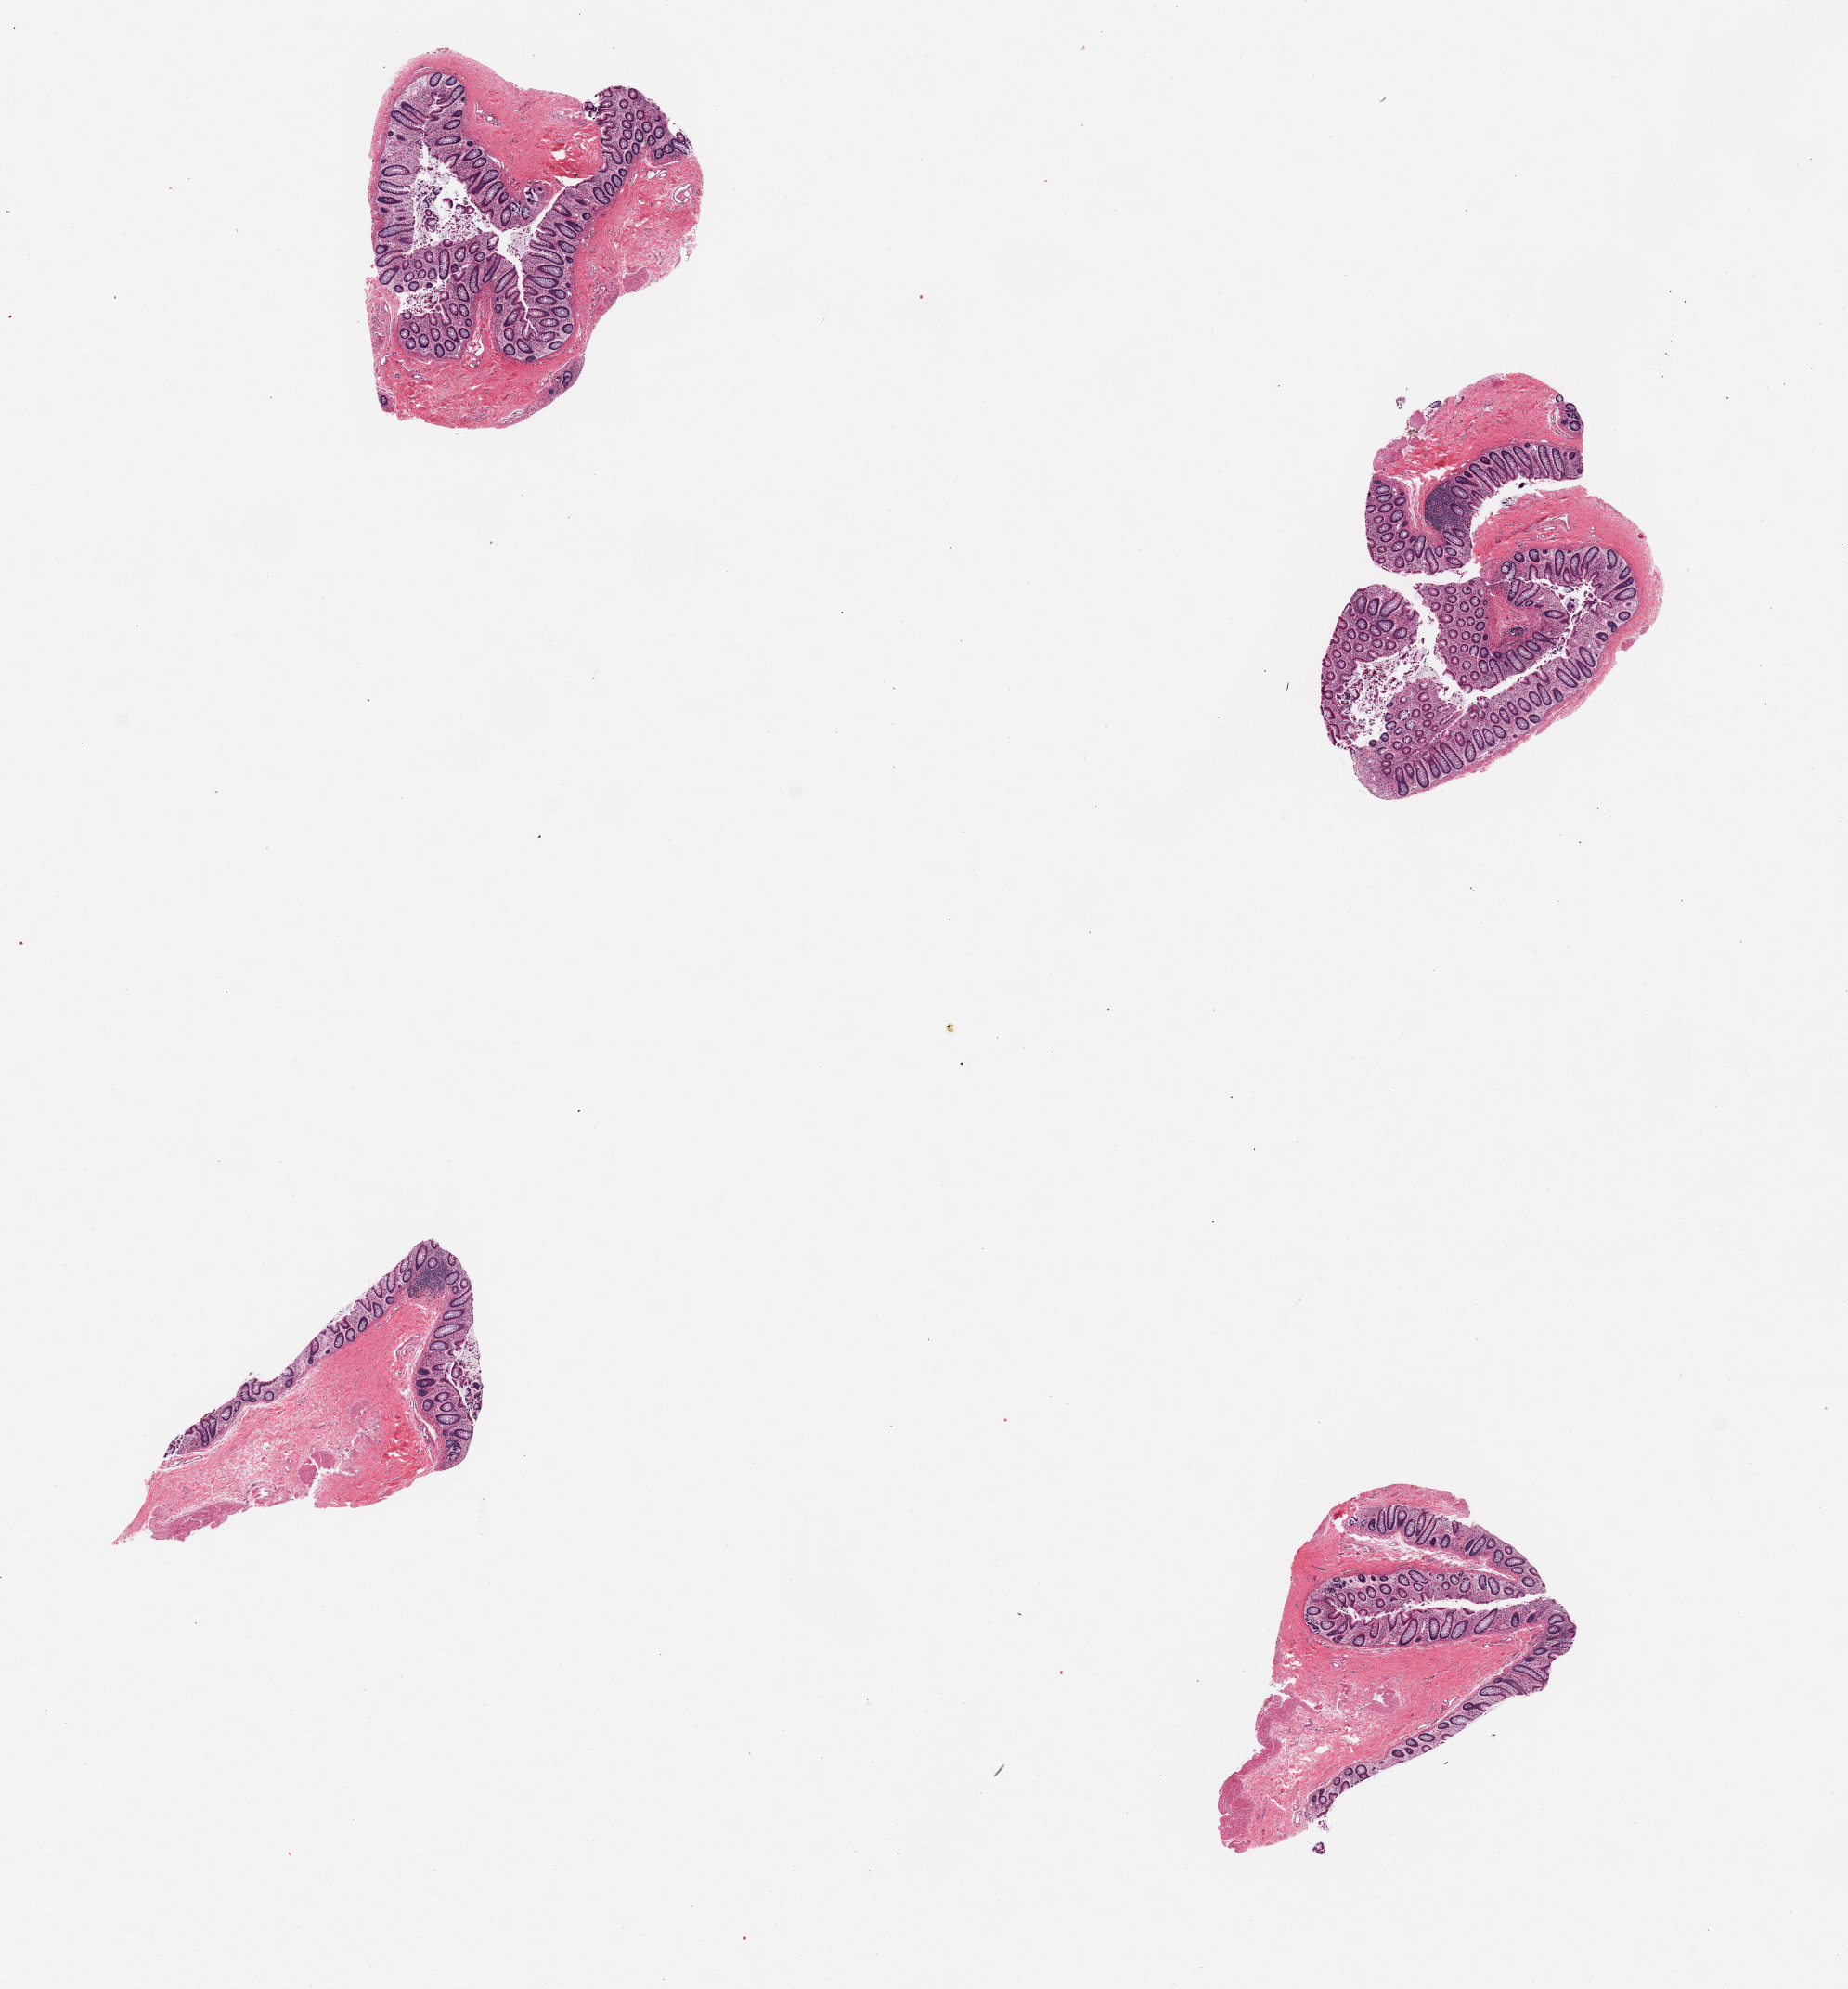
Whole-slide image, H&E stain, brightfield, low-resolution overview of the scanned area, about 15.8 x 17.0 mm (from a 20x scan); PAXgene-fixed, paraffin-embedded tissue; sampled site (target tissue): sigmoid colon; tissue donor sample. Female donor.
Pathologist's review note for this sample: 4 pieces, mucosa (not target).